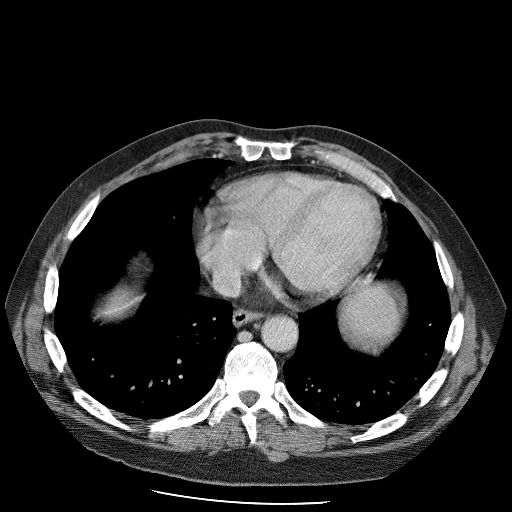
Contrast-enhanced abdominal CT (liver protocol), one axial slice; position 97 of 98 along the scan axis; reconstruction kernel STANDARD; 120 kVp; soft-tissue window (W 400 / L 40 HU); 2.5 mm slice thickness; 512 × 512 image matrix, field of view 400 × 400 mm. From the clinical record (not read from this slice): diagnosis: hepatocellular carcinoma (patient treated with transarterial chemoembolisation; whether this scan precedes or follows treatment is not stated here); TNM stage (as recorded): Stage-II; Child-Pugh class: B; tumour differentiation: moderately differentiated; tumour nodularity: uninodular.
Outlined on this slice (semi-automatic segmentation, software-assisted and operator-edited):
- liver parenchyma outside the tumour (the mass and vessels are separate outlines, so this box may not span the whole liver): bounding box <112,288,131,302> (left, top, right, bottom; pixels)